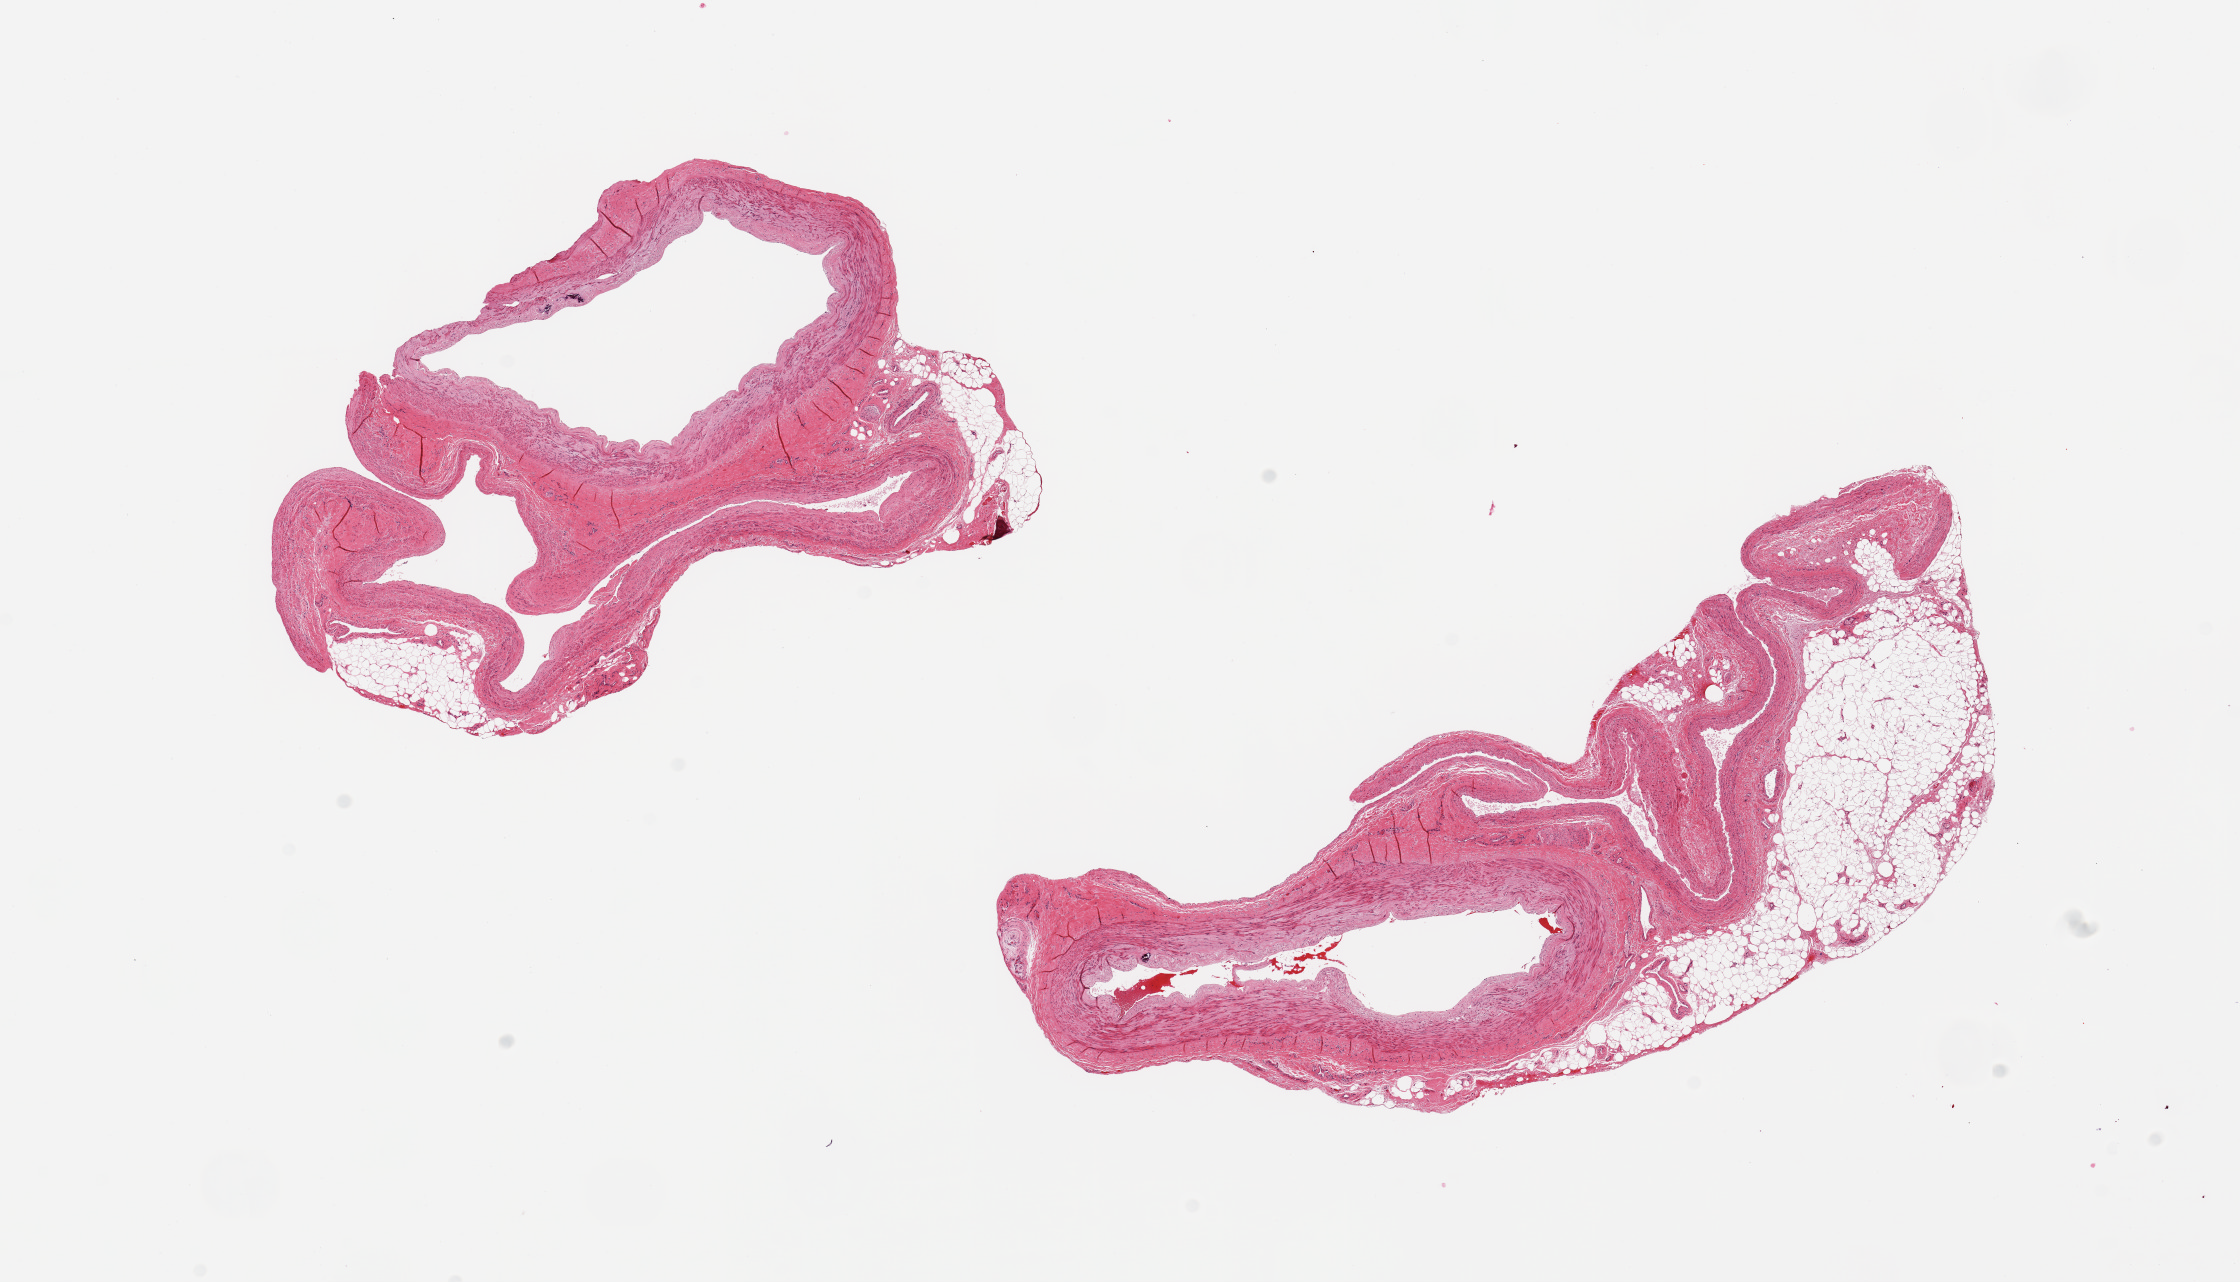
Whole-slide image, H&E stain, whole scanned area (about 17.7 x 10.1 mm, acquisition: 20x scan) shown as a low-resolution overview, PAXgene-fixed, paraffin-embedded tissue, sampled site (target tissue): tibial artery, tissue donor sample.
Pathologist's review note for this sample: 2 pieces, adherent fat up to ~2mm.